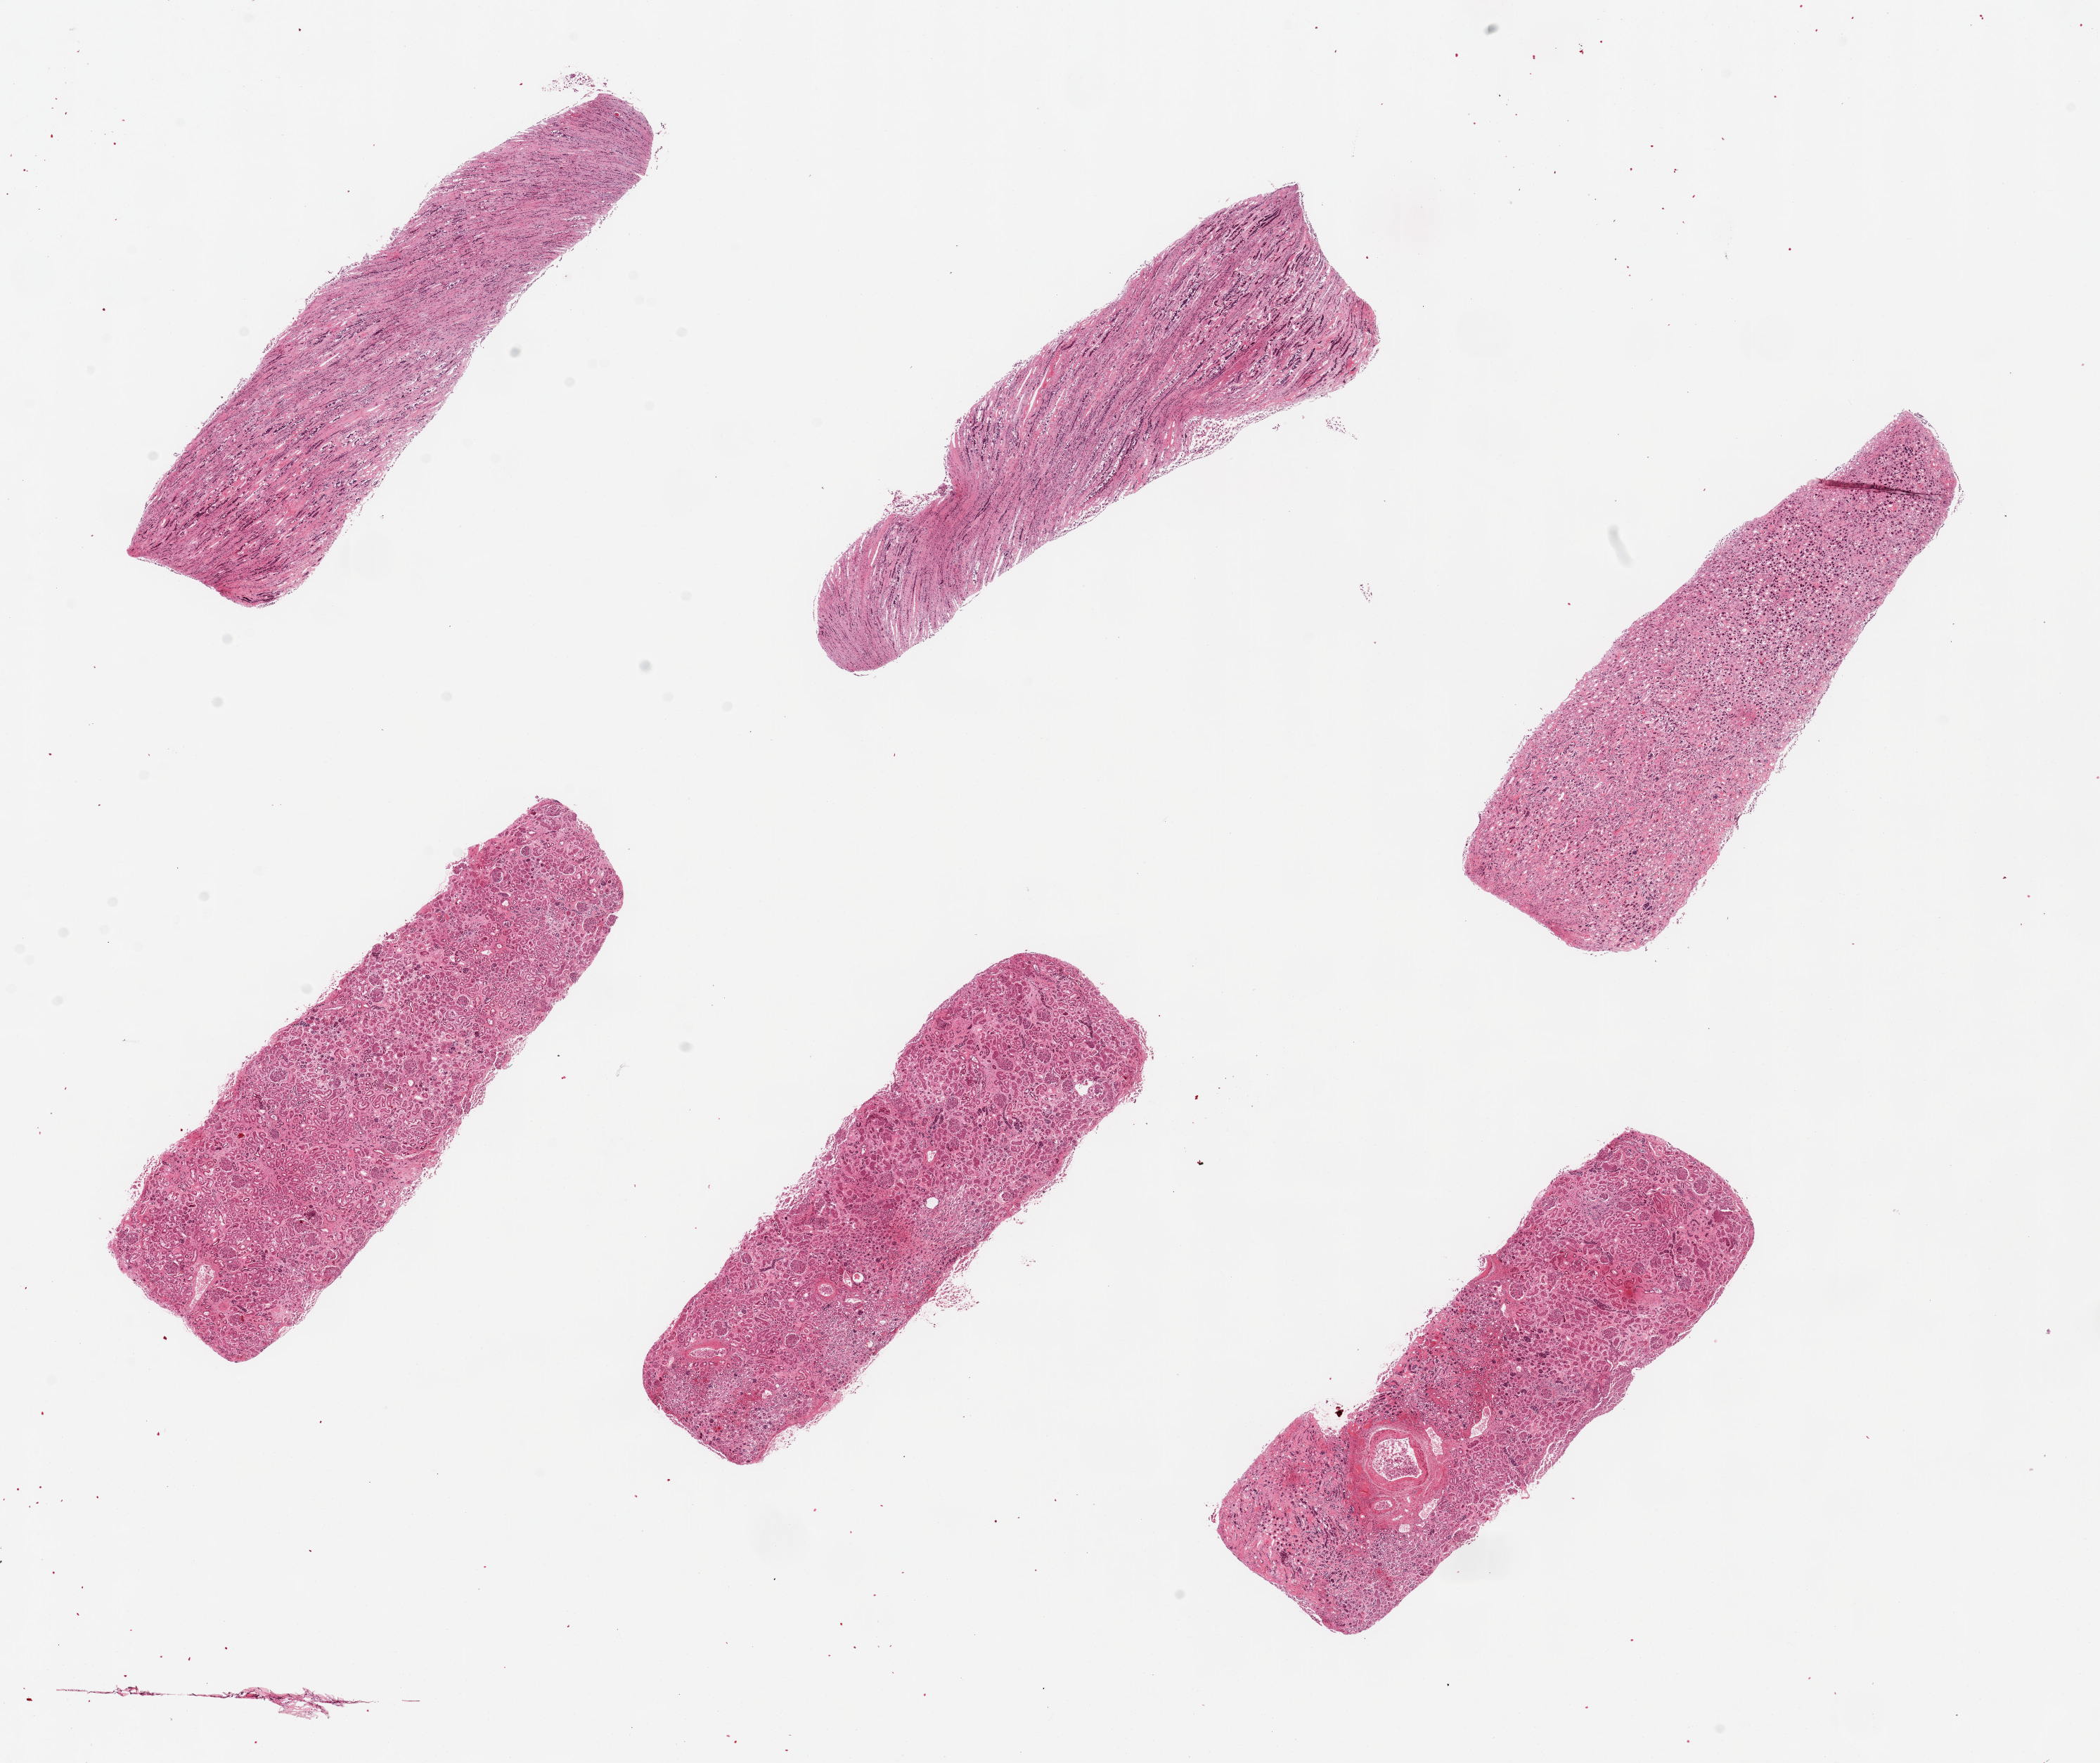
Whole-slide image, hematoxylin and eosin (H&E) stain, whole scanned area (about 23.6 x 19.8 mm, acquisition: 20x scan) shown as a low-resolution overview; PAXgene-fixed paraffin-embedded (PFPE) section; target tissue: renal cortex; tissue donor sample.
• review note (as recorded): 6 pieces, up to 7.5x2mm; 3 pieces are cortex (autolysis=2); 3 are medulla (autolysis=3)